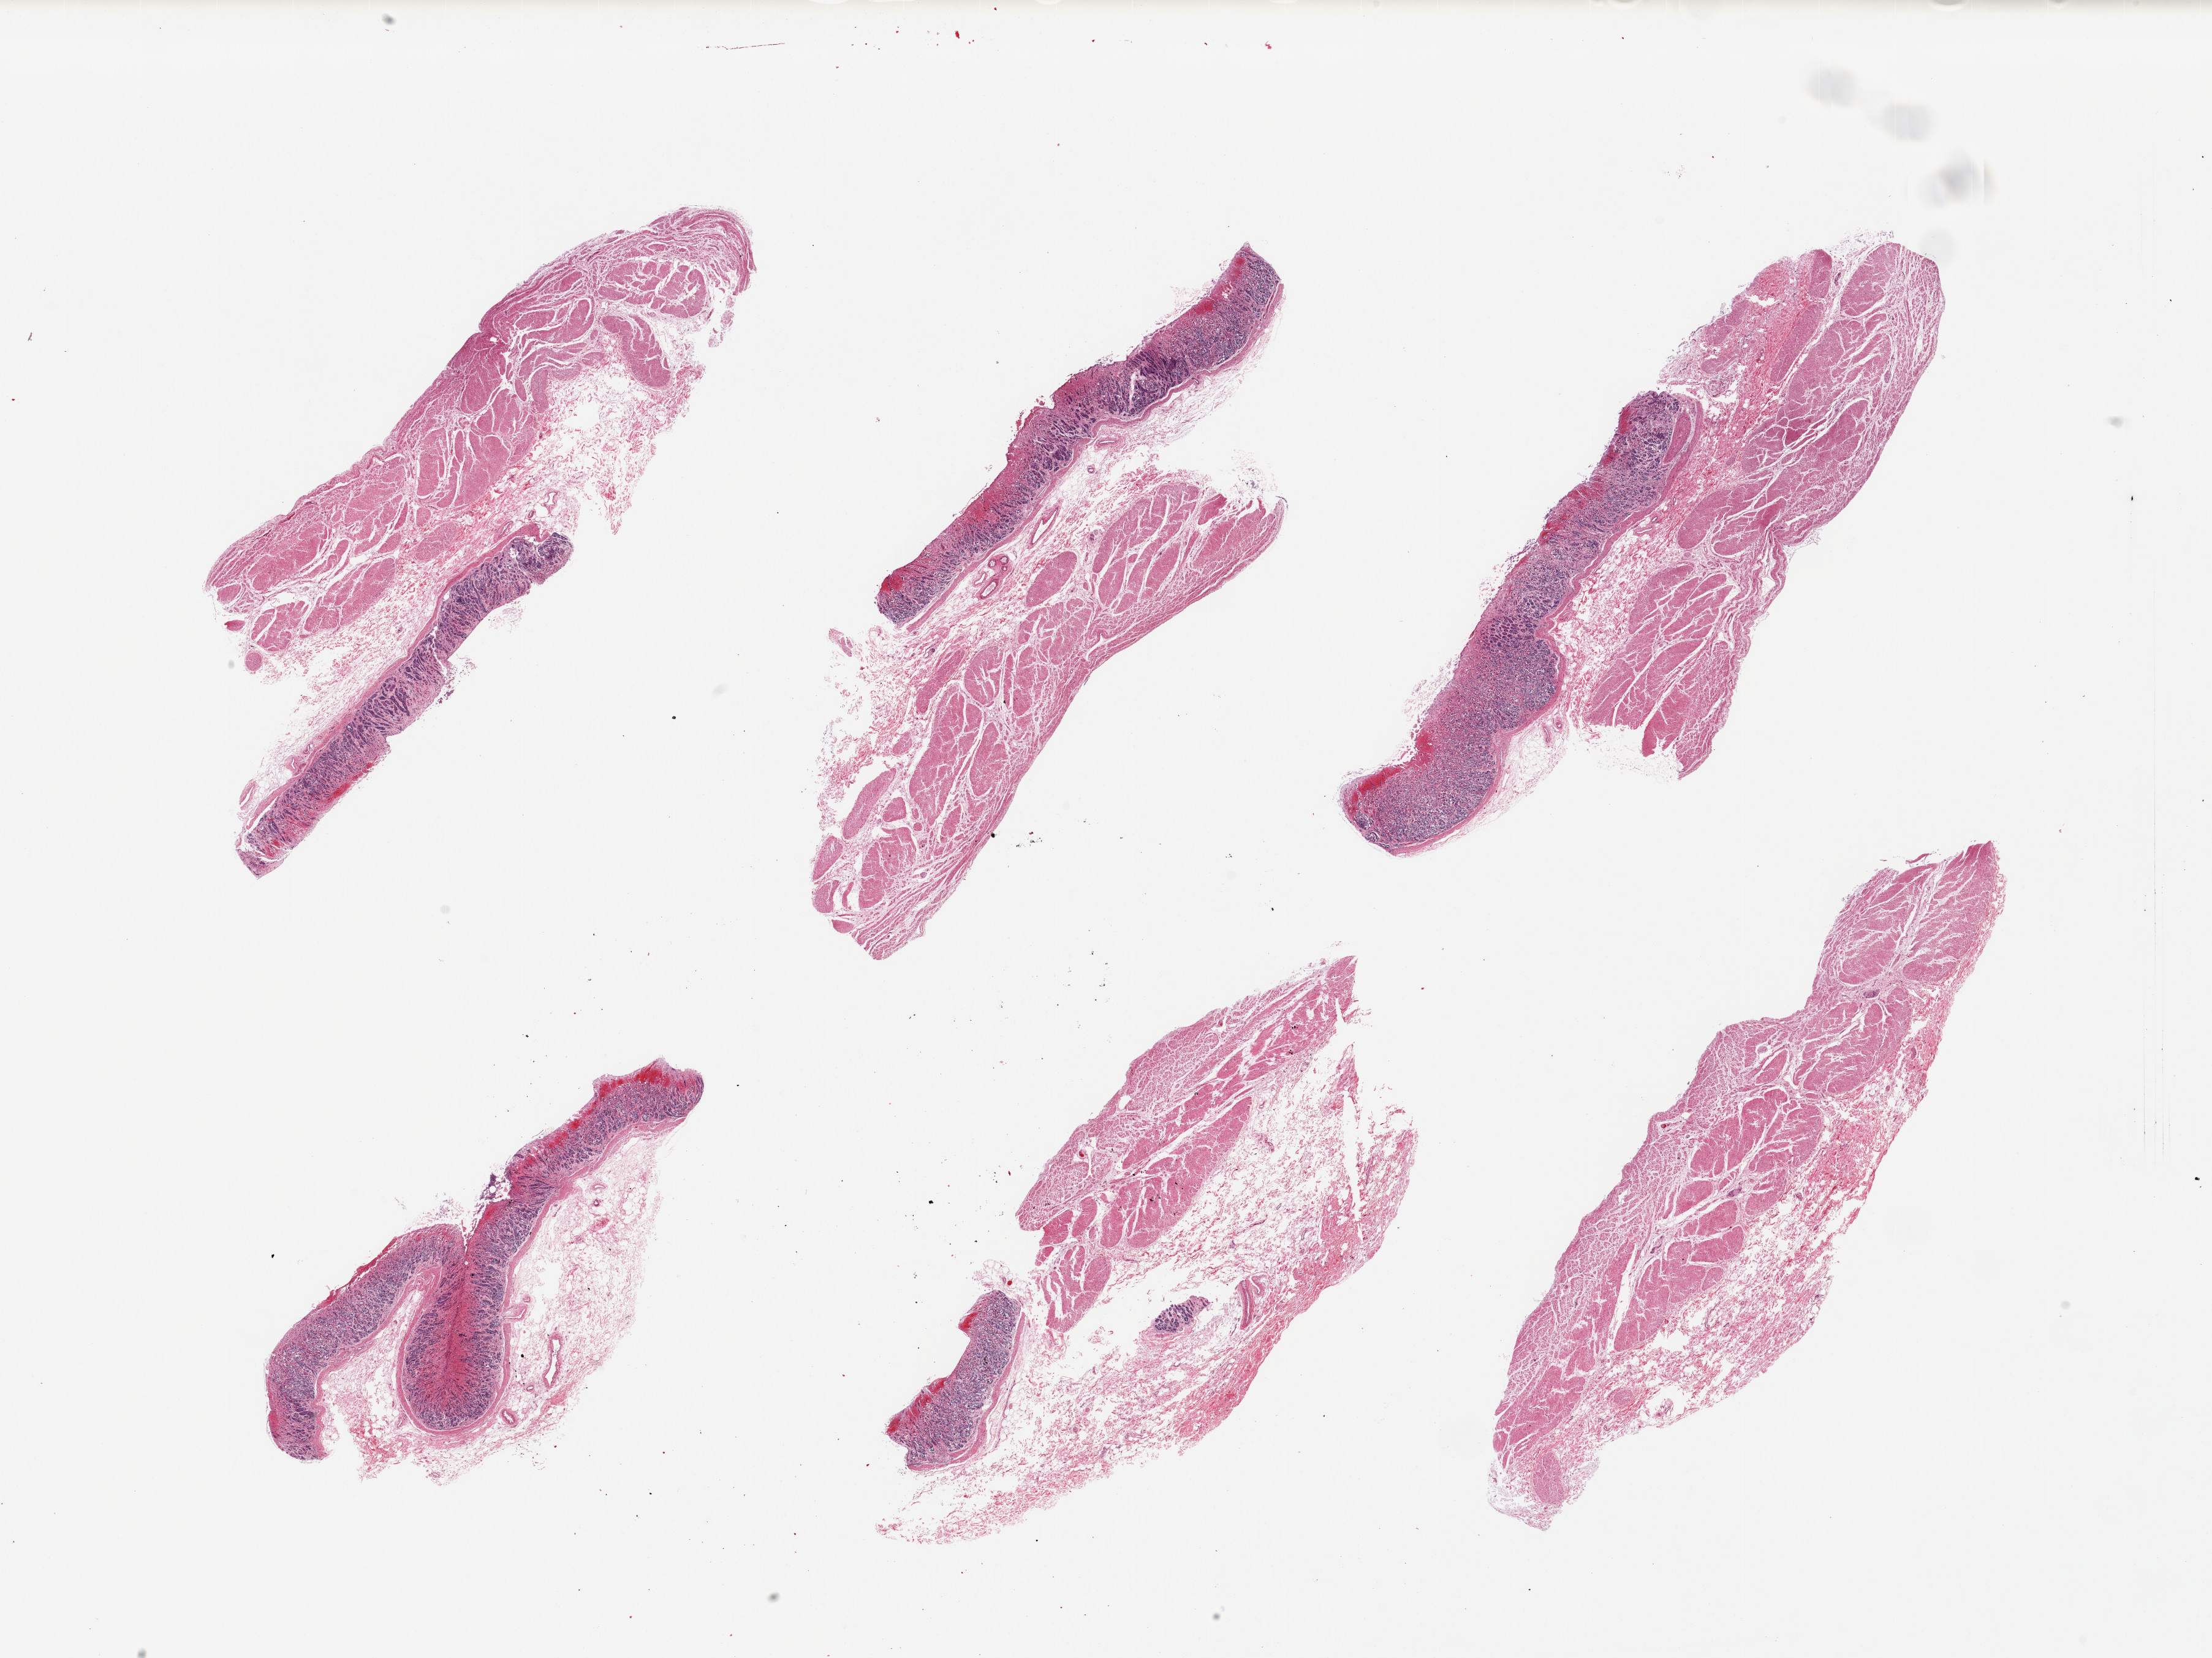
Digitized hematoxylin and eosin (H&E)-stained section, shown as a low-resolution overview of the whole scanned area (about 28.5 x 21.4 mm, acquisition: 20x scan). PAXgene-fixed, paraffin-embedded tissue. Section of stomach (target tissue). Donor tissue sample. Donor: male.
- pathologist's review note for this sample: 6 pieces; congestion and superficial mucosal fresh hemorrhage; 4 are full thickness, 1 mucosa only, 1 muscularis